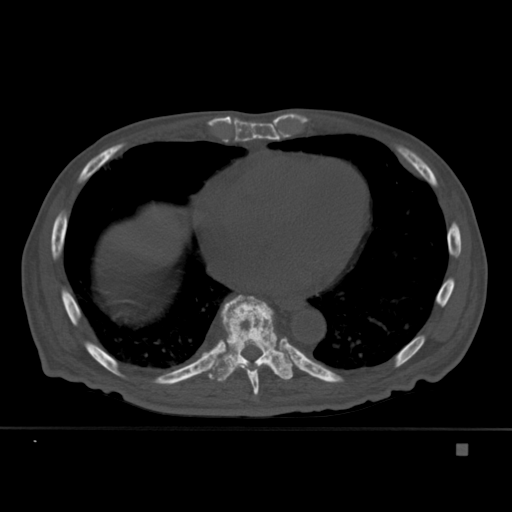
CT including the spine, one axial slice. Position 253 of 451 along the scan axis. Bone window (W 1800 / L 400 HU). 512 × 512 image matrix, field of view 378 × 378 mm. Patient: male, 75 years. From the clinical record (not read from this slice): primary cancer: prostate.
Annotated regions visible in this slice (semi-automatic segmentation, software-assisted and operator-edited):
- T8 vertebra: bounding box [x1, y1, x2, y2] px = [227, 337, 269, 395]
- T9 vertebra: [205, 295, 293, 382]